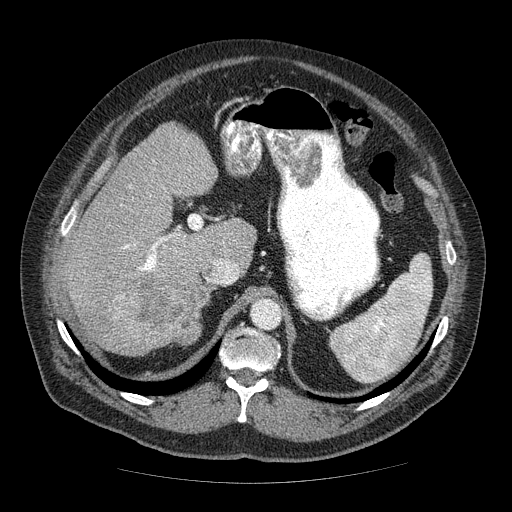
Contrast-enhanced abdominal CT (liver protocol), one axial slice; slice 38 of 85 in the series (ordered by position); reconstruction kernel STANDARD; soft-tissue window (W 400 / L 40 HU); 2.5 mm slice thickness; 512 × 512 image matrix, field of view 420 × 420 mm. From the clinical record (not read from this slice): diagnosis: hepatocellular carcinoma (patient treated with transarterial chemoembolisation; whether this scan precedes or follows treatment is not stated here); TNM stage (as recorded): Stage-IIIA; Child-Pugh class: A; tumour size: 7 cm.
Structures marked on this image (semi-automatic segmentation, software-assisted and operator-edited):
- liver parenchyma outside the tumour (the mass and vessels are separate outlines, so this box may not span the whole liver): box from (x=64, y=123) to (x=256, y=354) px
- mass: (x=86, y=274)–(x=202, y=355)
- liver vessels: (x=122, y=186)–(x=179, y=271)